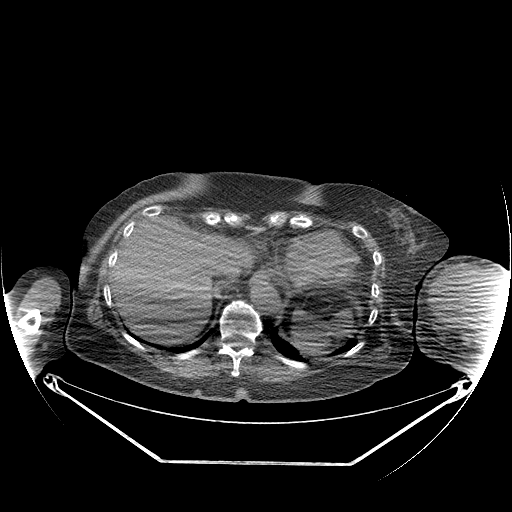
CT of an extremity soft-tissue mass (from a PET/CT study), one axial slice; position 142 of 267 along the scan axis; reconstruction kernel STANDARD; soft-tissue window (W 400 / L 40 HU); 512 × 512 image matrix, field of view 500 × 500 mm. Female patient. From the clinical record (not read from this slice): histological type: pleiomorphic leiomyosarcoma; grade: high; site of the primary tumour: left biceps.
Structures marked on this image (expert contour drawn on MRI and transferred to this co-registered scan by the dataset authors):
- gross tumour volume including surrounding oedema: bounding box [x1, y1, x2, y2] px = [441, 272, 501, 321]
- gross tumour volume (mass): [441, 272, 497, 309]